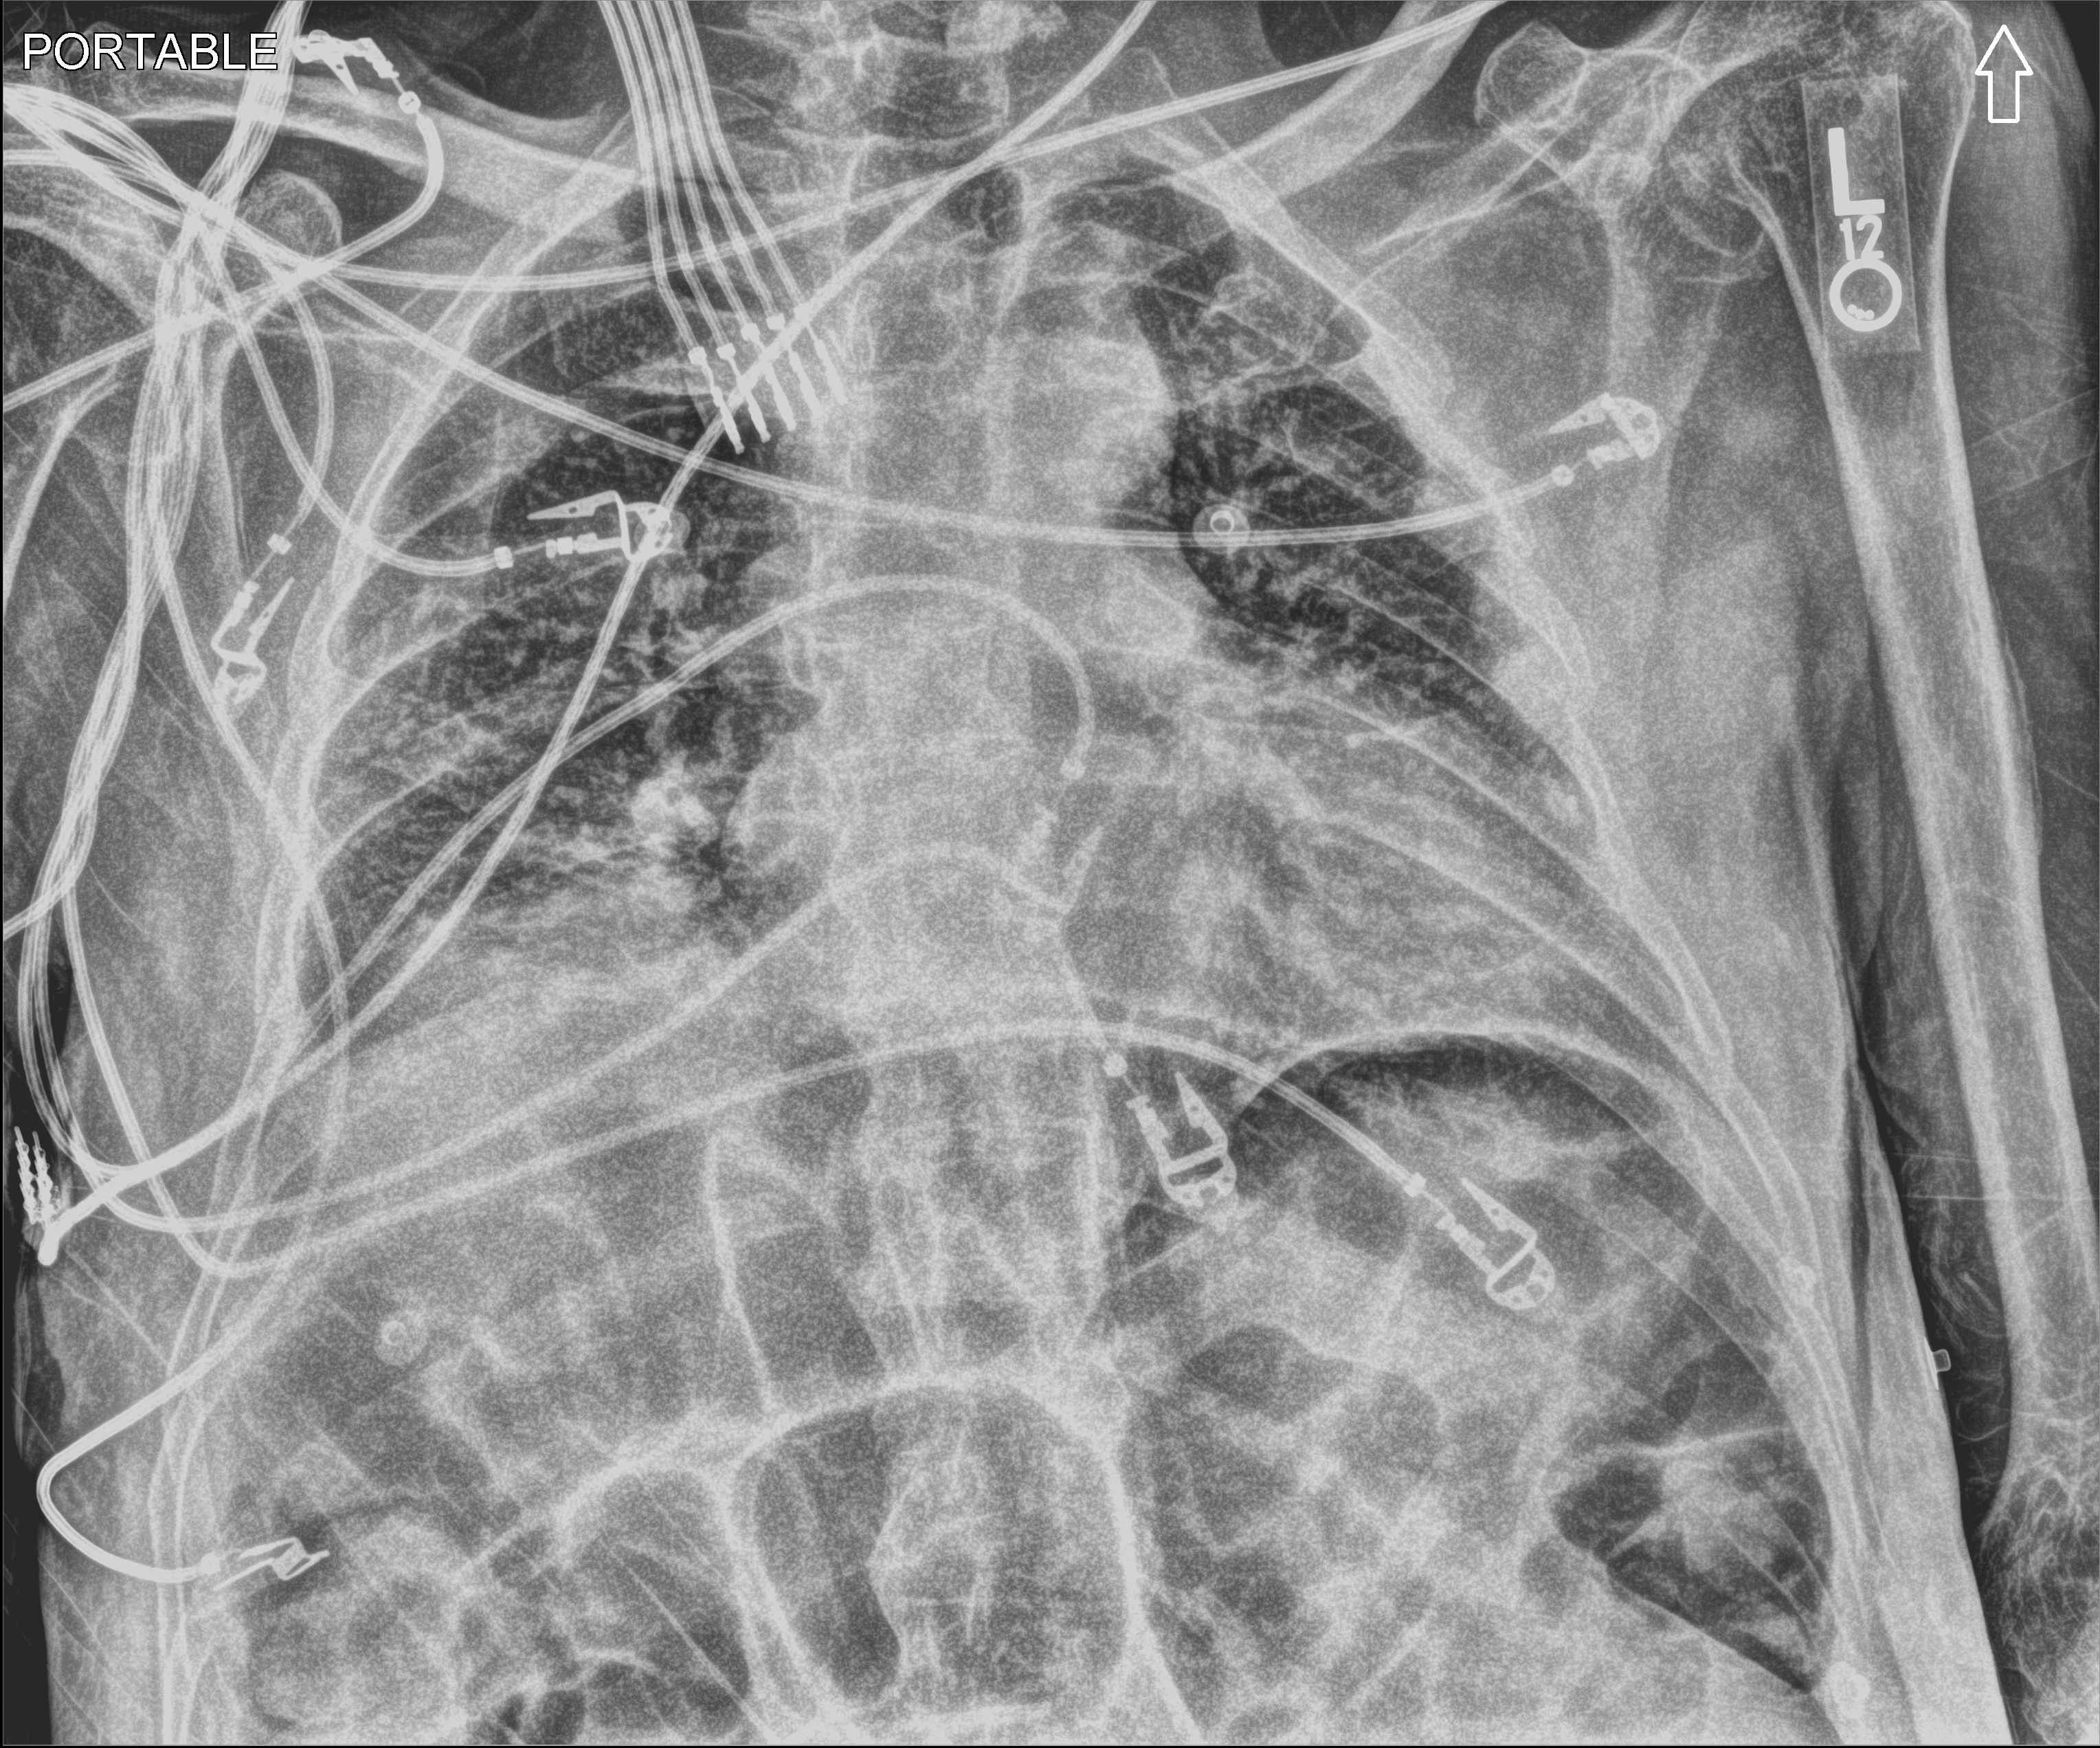
Bedside chest radiograph (computed radiography), anteroposterior (AP) projection. Patient hospitalised with COVID-19; male, aged 75–90 years.
From the hospital-stay record, not from the radiograph (when in the stay this image was taken is not recorded):
- mechanically ventilated during this hospital stay: no
- admitted to intensive care during this hospital stay: no